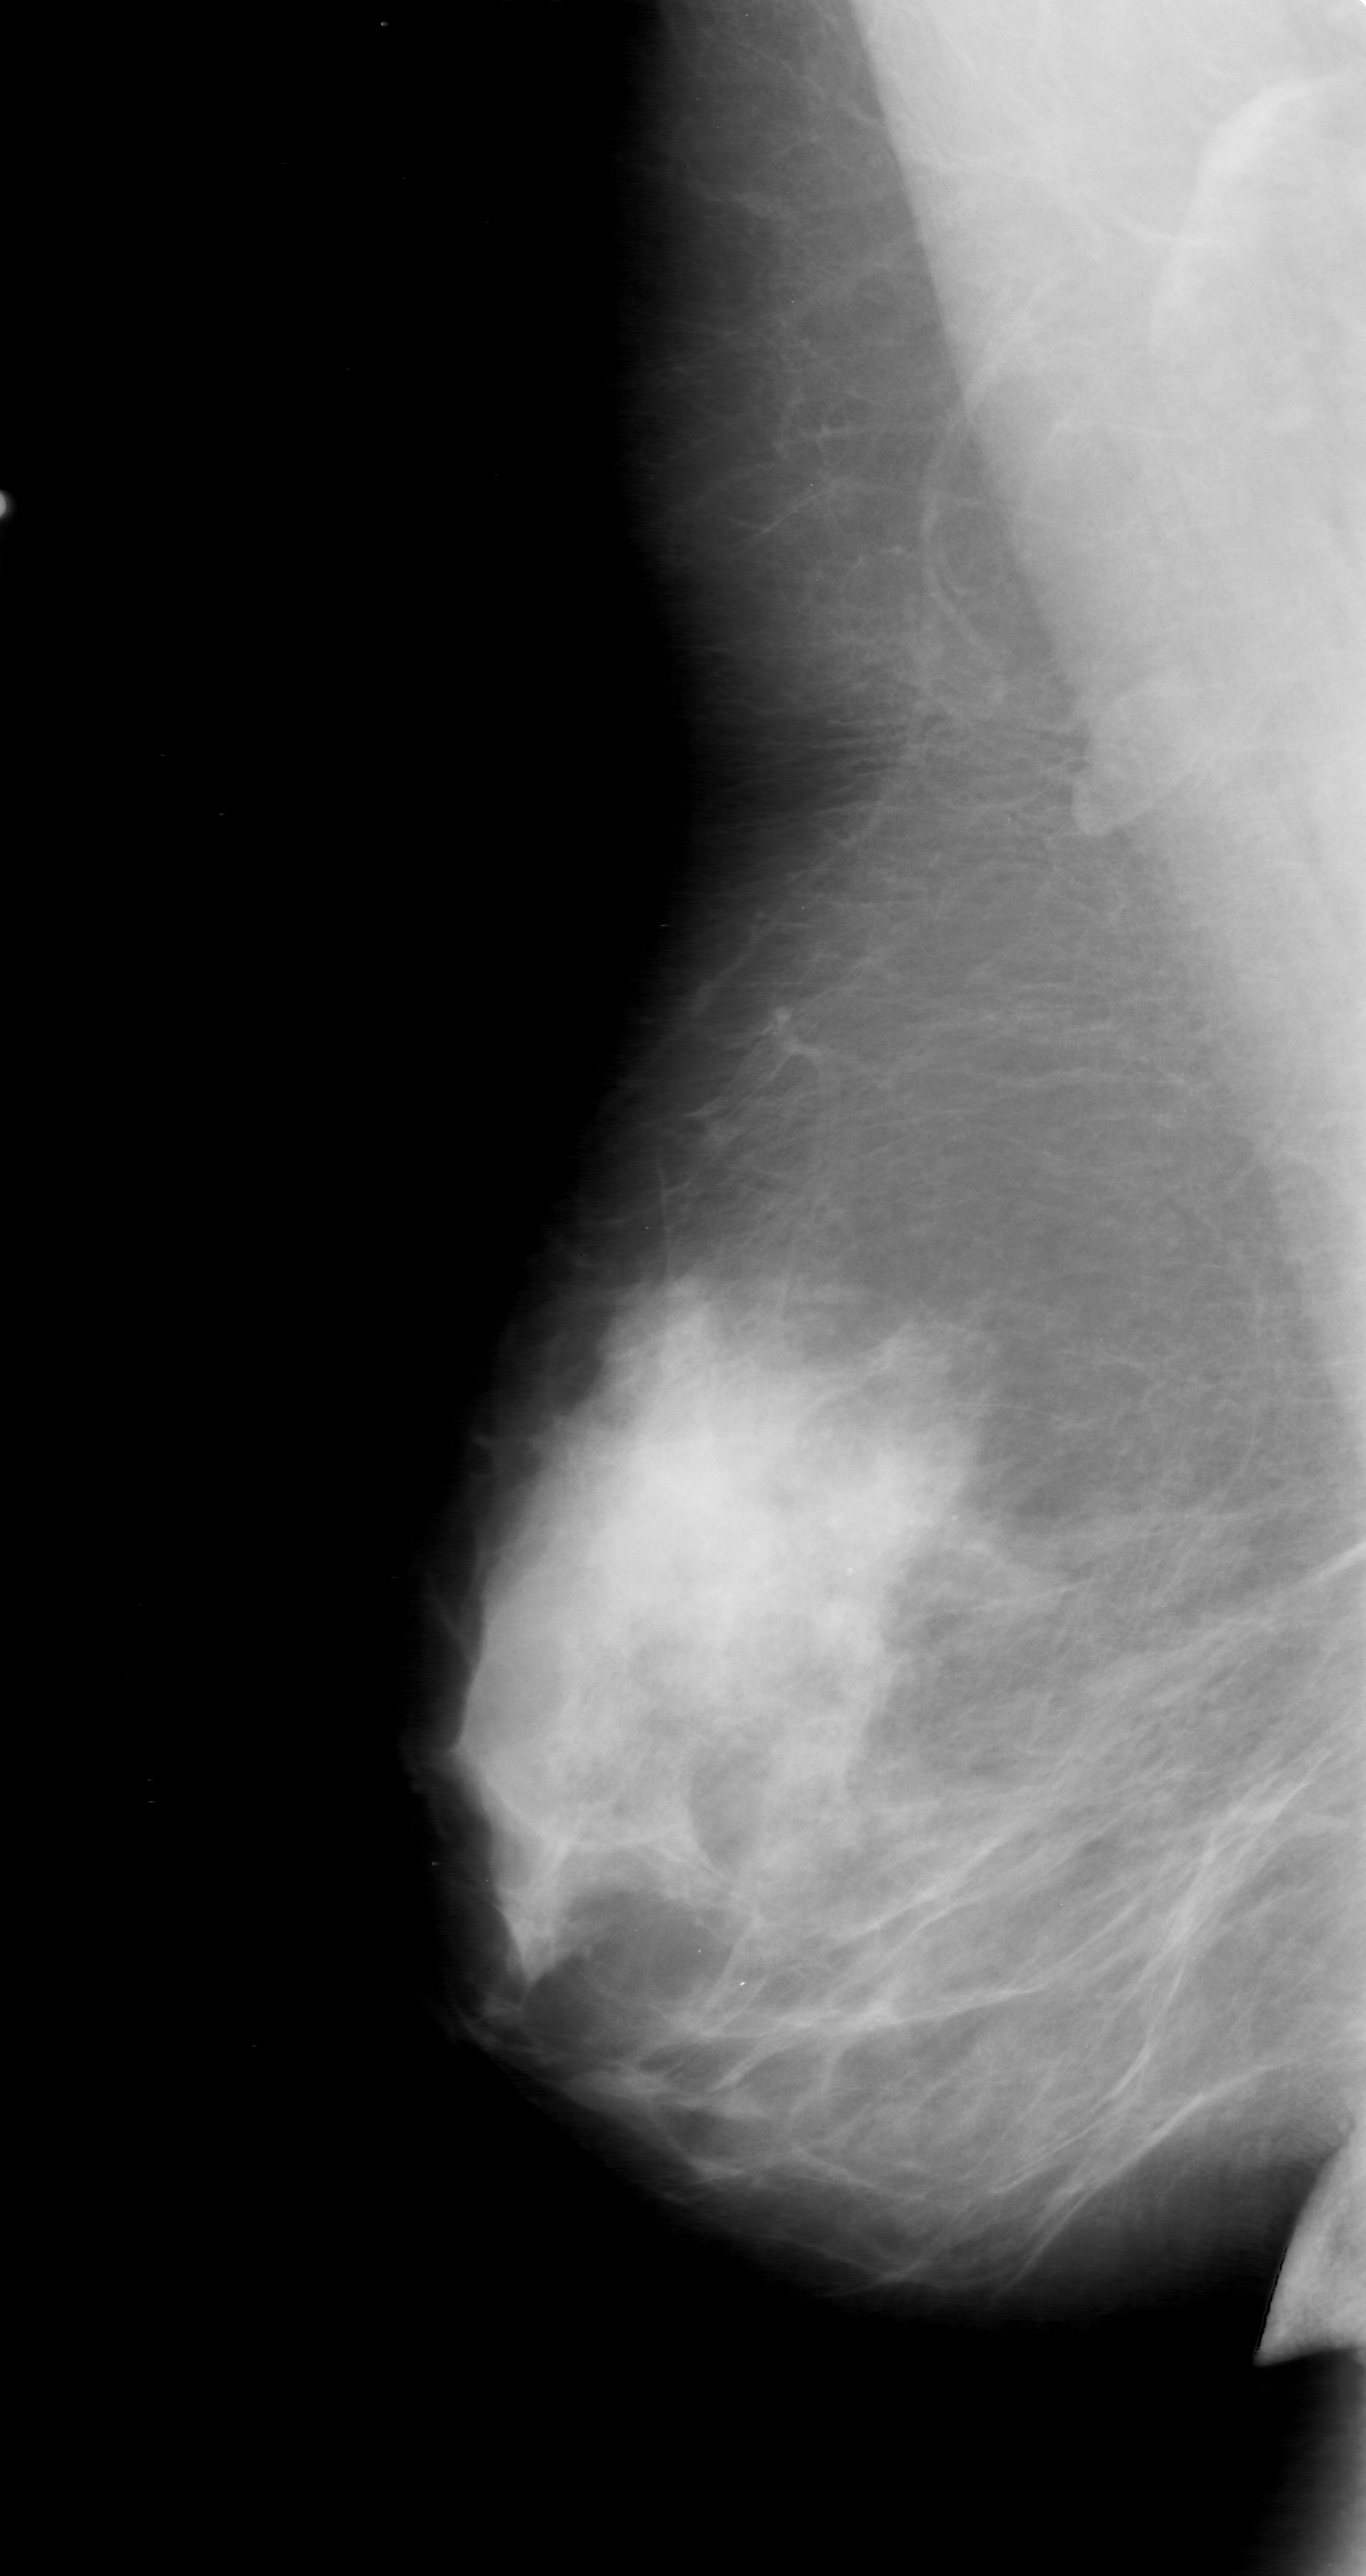
Mammogram (digitized film); right breast; mediolateral oblique (MLO) view; breast composition: heterogeneously dense (BI-RADS density category 3 of 4); 1366 × 2576 image matrix.
Marked abnormalities (boxes around the expert regions of interest):
- calcifications, morphology pleomorphic, distribution clustered; BI-RADS assessment category 0; pathology (as recorded): malignant: bounding box (x1, y1, x2, y2) in pixels: (669, 1383, 1070, 1703)